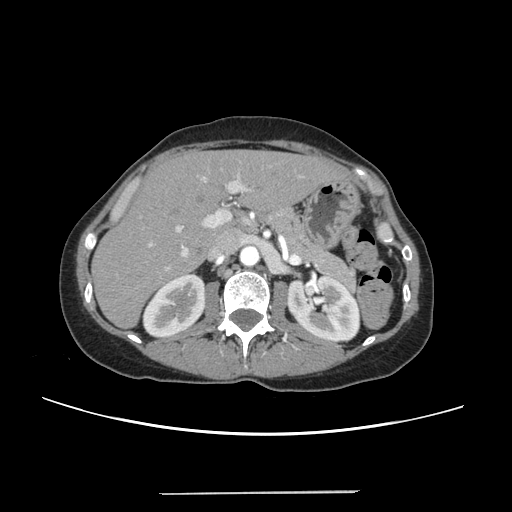
Contrast-enhanced abdominal CT, one axial slice; slice 142 of 240 in the series (ordered by position); intravenous contrast given; soft-tissue window (W 400 / L 40 HU); 512 × 512 image matrix, field of view 371 × 371 mm. Female patient, age 60 years. From the clinical record (not read from this slice): diagnosis: colorectal cancer liver metastases, imaged before liver resection; multiple liver metastases: no; largest metastasis: 1.5 cm.
Structures marked on this image (manually delineated by an expert):
- liver: bounding box (x1, y1, x2, y2) in pixels: (94, 151, 344, 326)
- planned liver remnant (the part of the liver to remain after resection): (94, 151, 344, 326)
- portal vein (with intrahepatic branches): (142, 168, 300, 270)